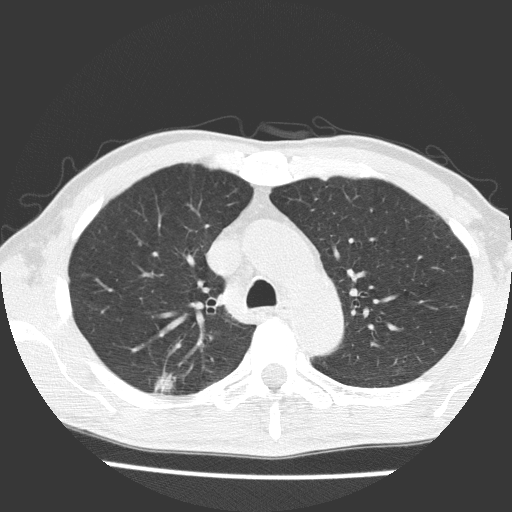
Low-dose screening chest CT, axial slice, baseline annual screen, lung window (W 1500 / L -600 HU). Male, age 66 years at enrolment. Current smoker at enrolment.
• Lesion marked by an expert reader, bounding box <141,360,192,409> (left, top, right, bottom; pixels).
• Screening reader's record for this exam (one nodule recorded; not confirmed to be the boxed lesion): non-calcified nodule or mass ≥4 mm, right upper lobe, 15 × 10 mm, spiculated (stellate) margins, soft tissue attenuation.
• Lung cancer was diagnosed 43 days after this screen: adenocarcinoma, NOS, right upper lobe, moderately differentiated (G2), stage IB (AJCC 6th edition), 11 mm at pathology.